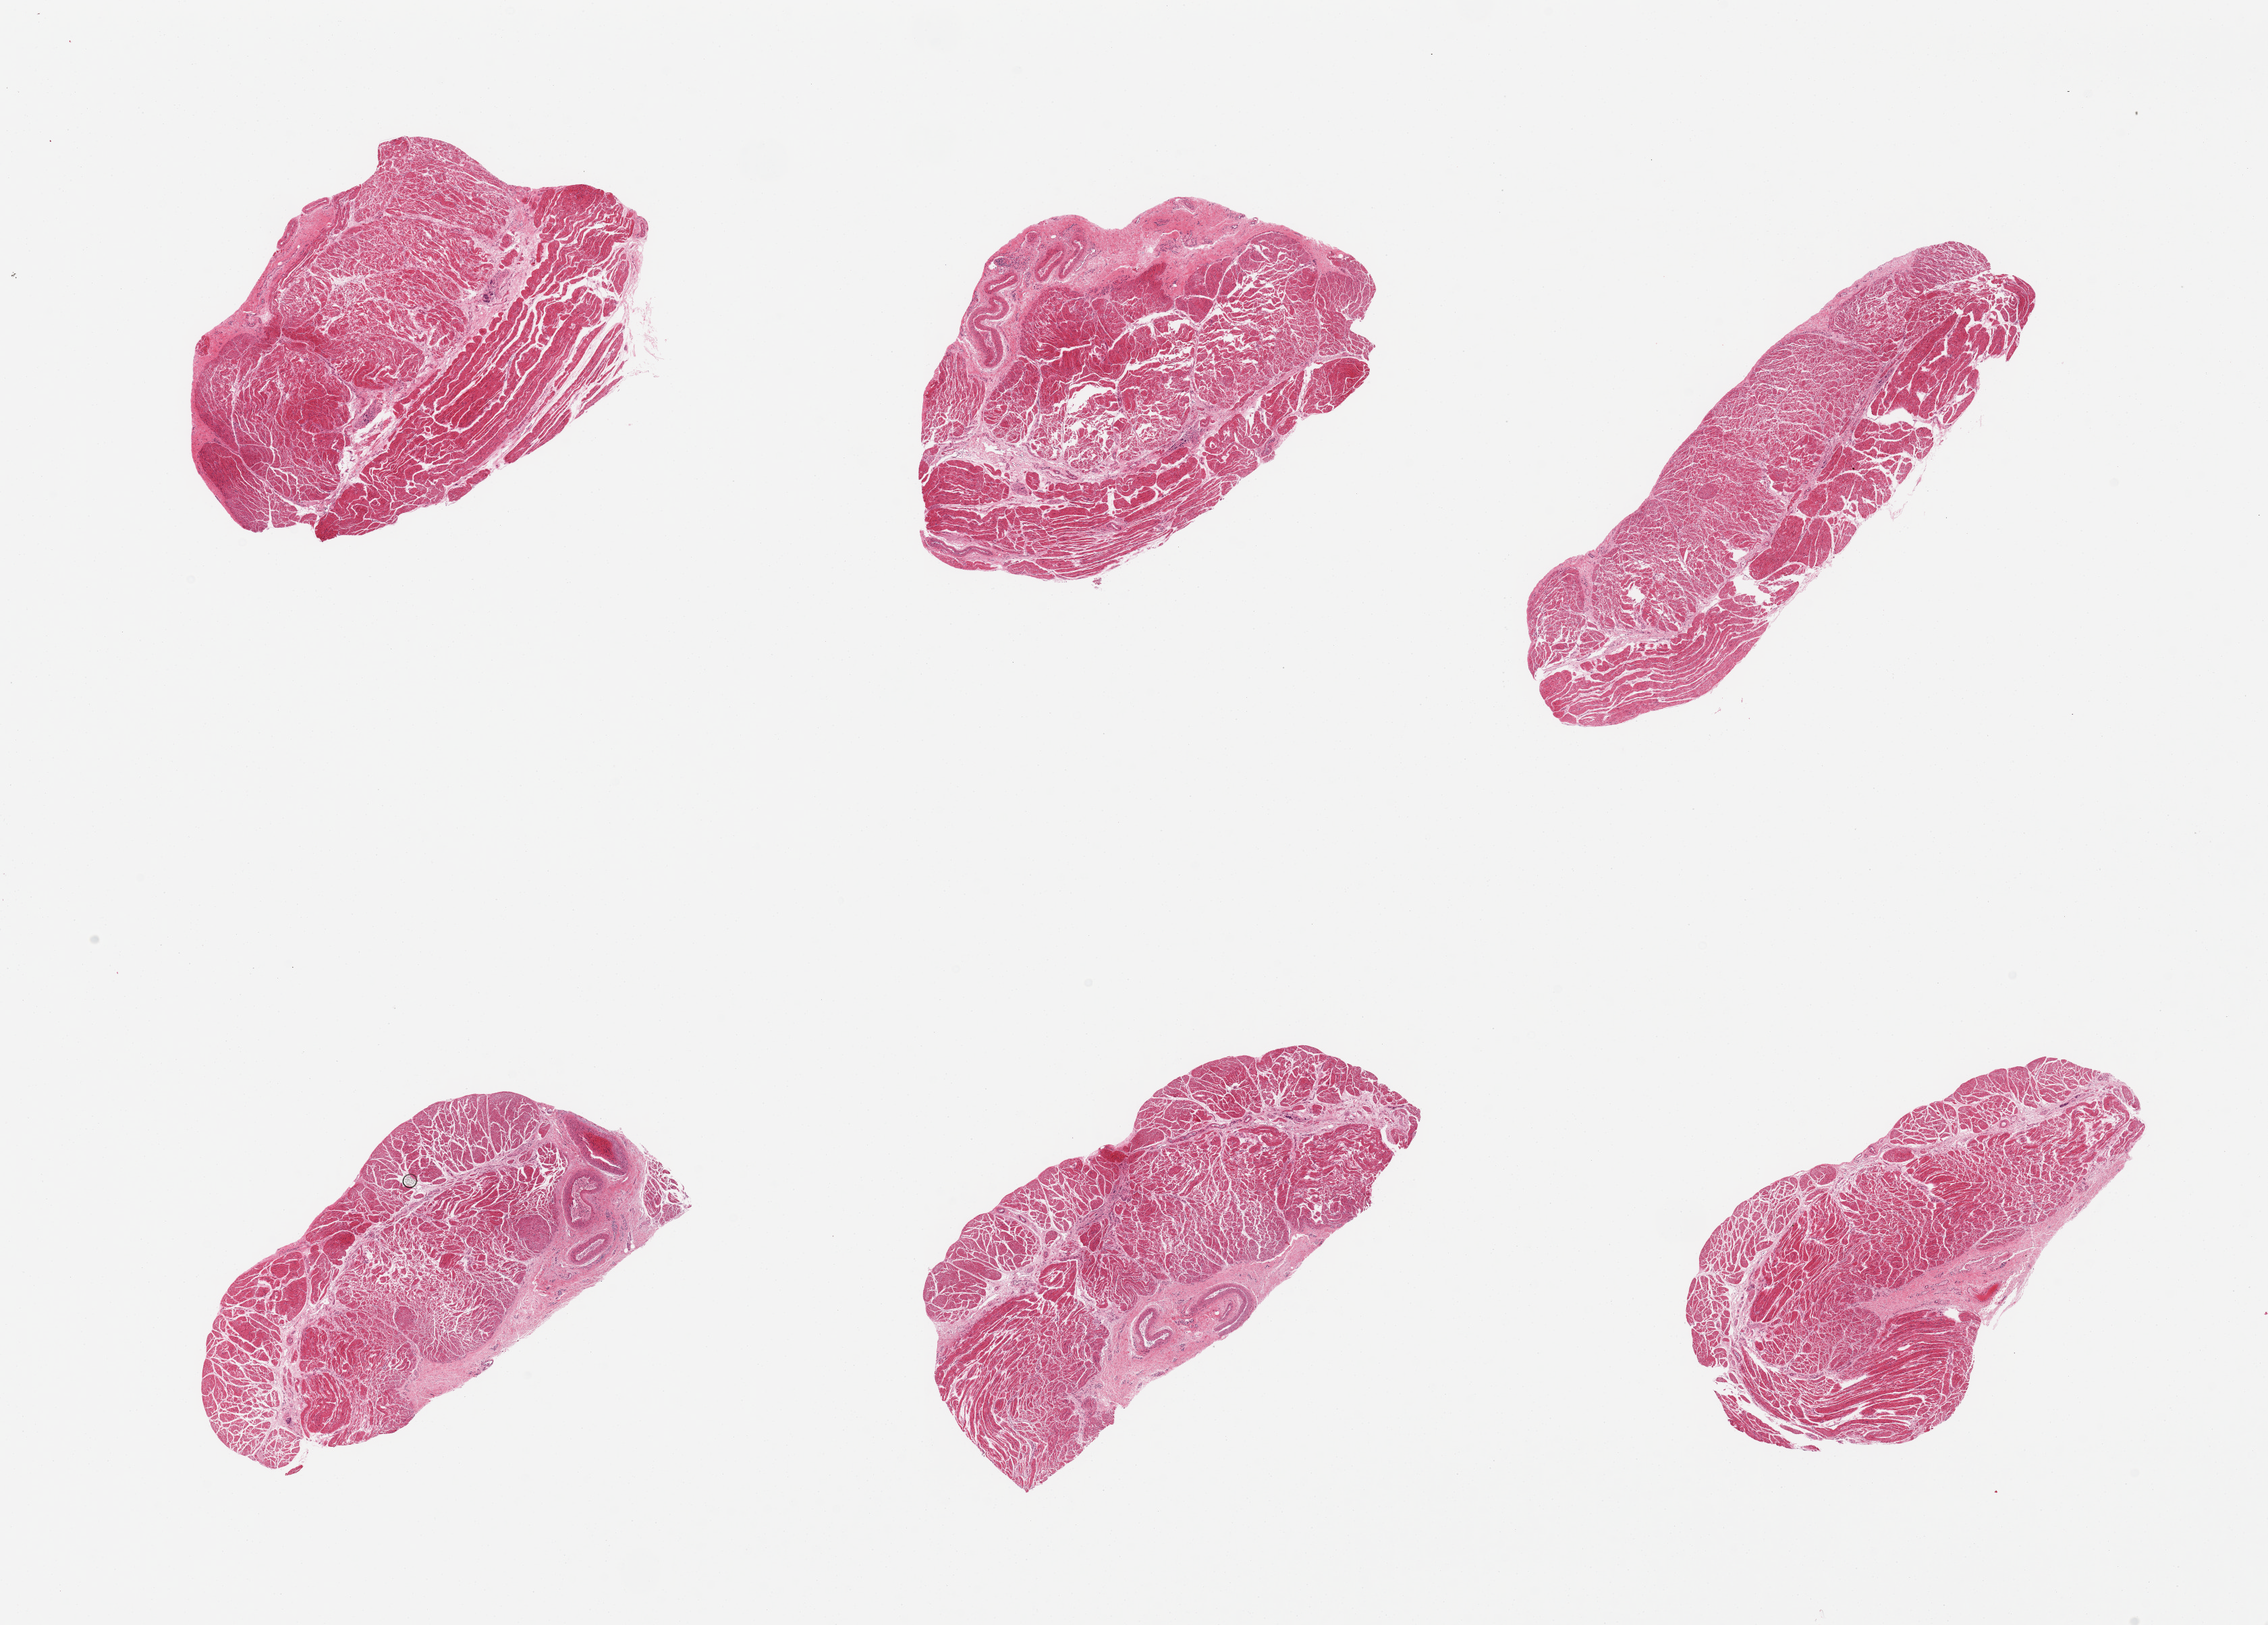
Digitized hematoxylin and eosin (H&E)-stained section, brightfield, whole scanned area (about 26.6 x 19.0 mm, slide scanned at 20x) shown as a low-resolution overview, PAXgene-fixed paraffin-embedded (PFPE) section, section of gastroesophageal junction (target tissue), tissue donor sample. Male donor.
• review note (as recorded): 6 pieces, all muscularis